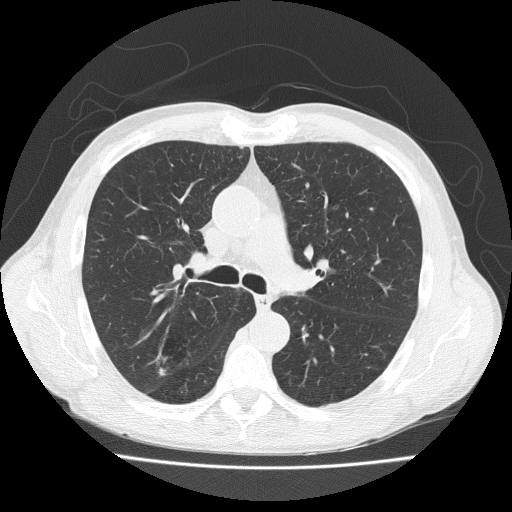
Axial slice from a low-dose chest CT screening exam, baseline annual screen, lung window (W 1500 / L -600 HU), 2 mm slice thickness, lung (sharp) reconstruction kernel (FC51), 512 × 512 image matrix, field of view 370 × 370 mm. Male participant, aged 73 years at enrolment. Current smoker at enrolment.
Expert reader's lesion annotation, box from (x=144, y=330) to (x=193, y=376) px. No non-calcified nodule or mass ≥4 mm was recorded by the screening reader at this exam. Participant outcome: lung cancer diagnosed 777 days after this screen — adenosquamous carcinoma, right upper lobe, well differentiated (G1), stage IA (AJCC 6th edition), 20 mm at pathology.